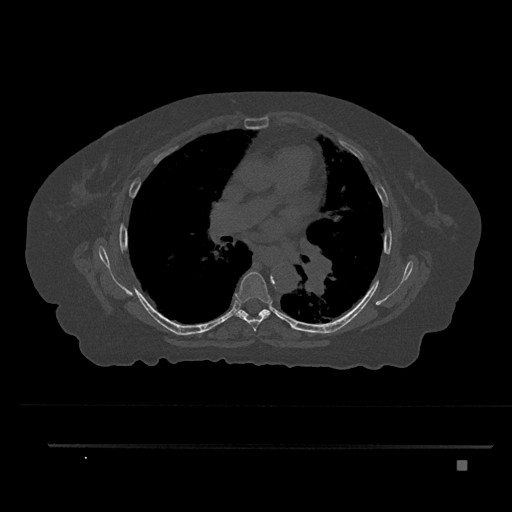
CT including the spine, one axial slice; slice 515 of 797 in the series (ordered by position); bone window (W 1800 / L 400 HU); 0.5 mm slice thickness; 512 × 512 image matrix, field of view 437 × 437 mm. Female patient, age 76 years. From the clinical record (not read from this slice): primary cancer: lung.
Structures marked on this image (semi-automatic segmentation, software-assisted and operator-edited):
- T6 vertebra: bounding box [x1, y1, x2, y2] px = [235, 271, 271, 331]
- T7 vertebra: [238, 309, 270, 317]